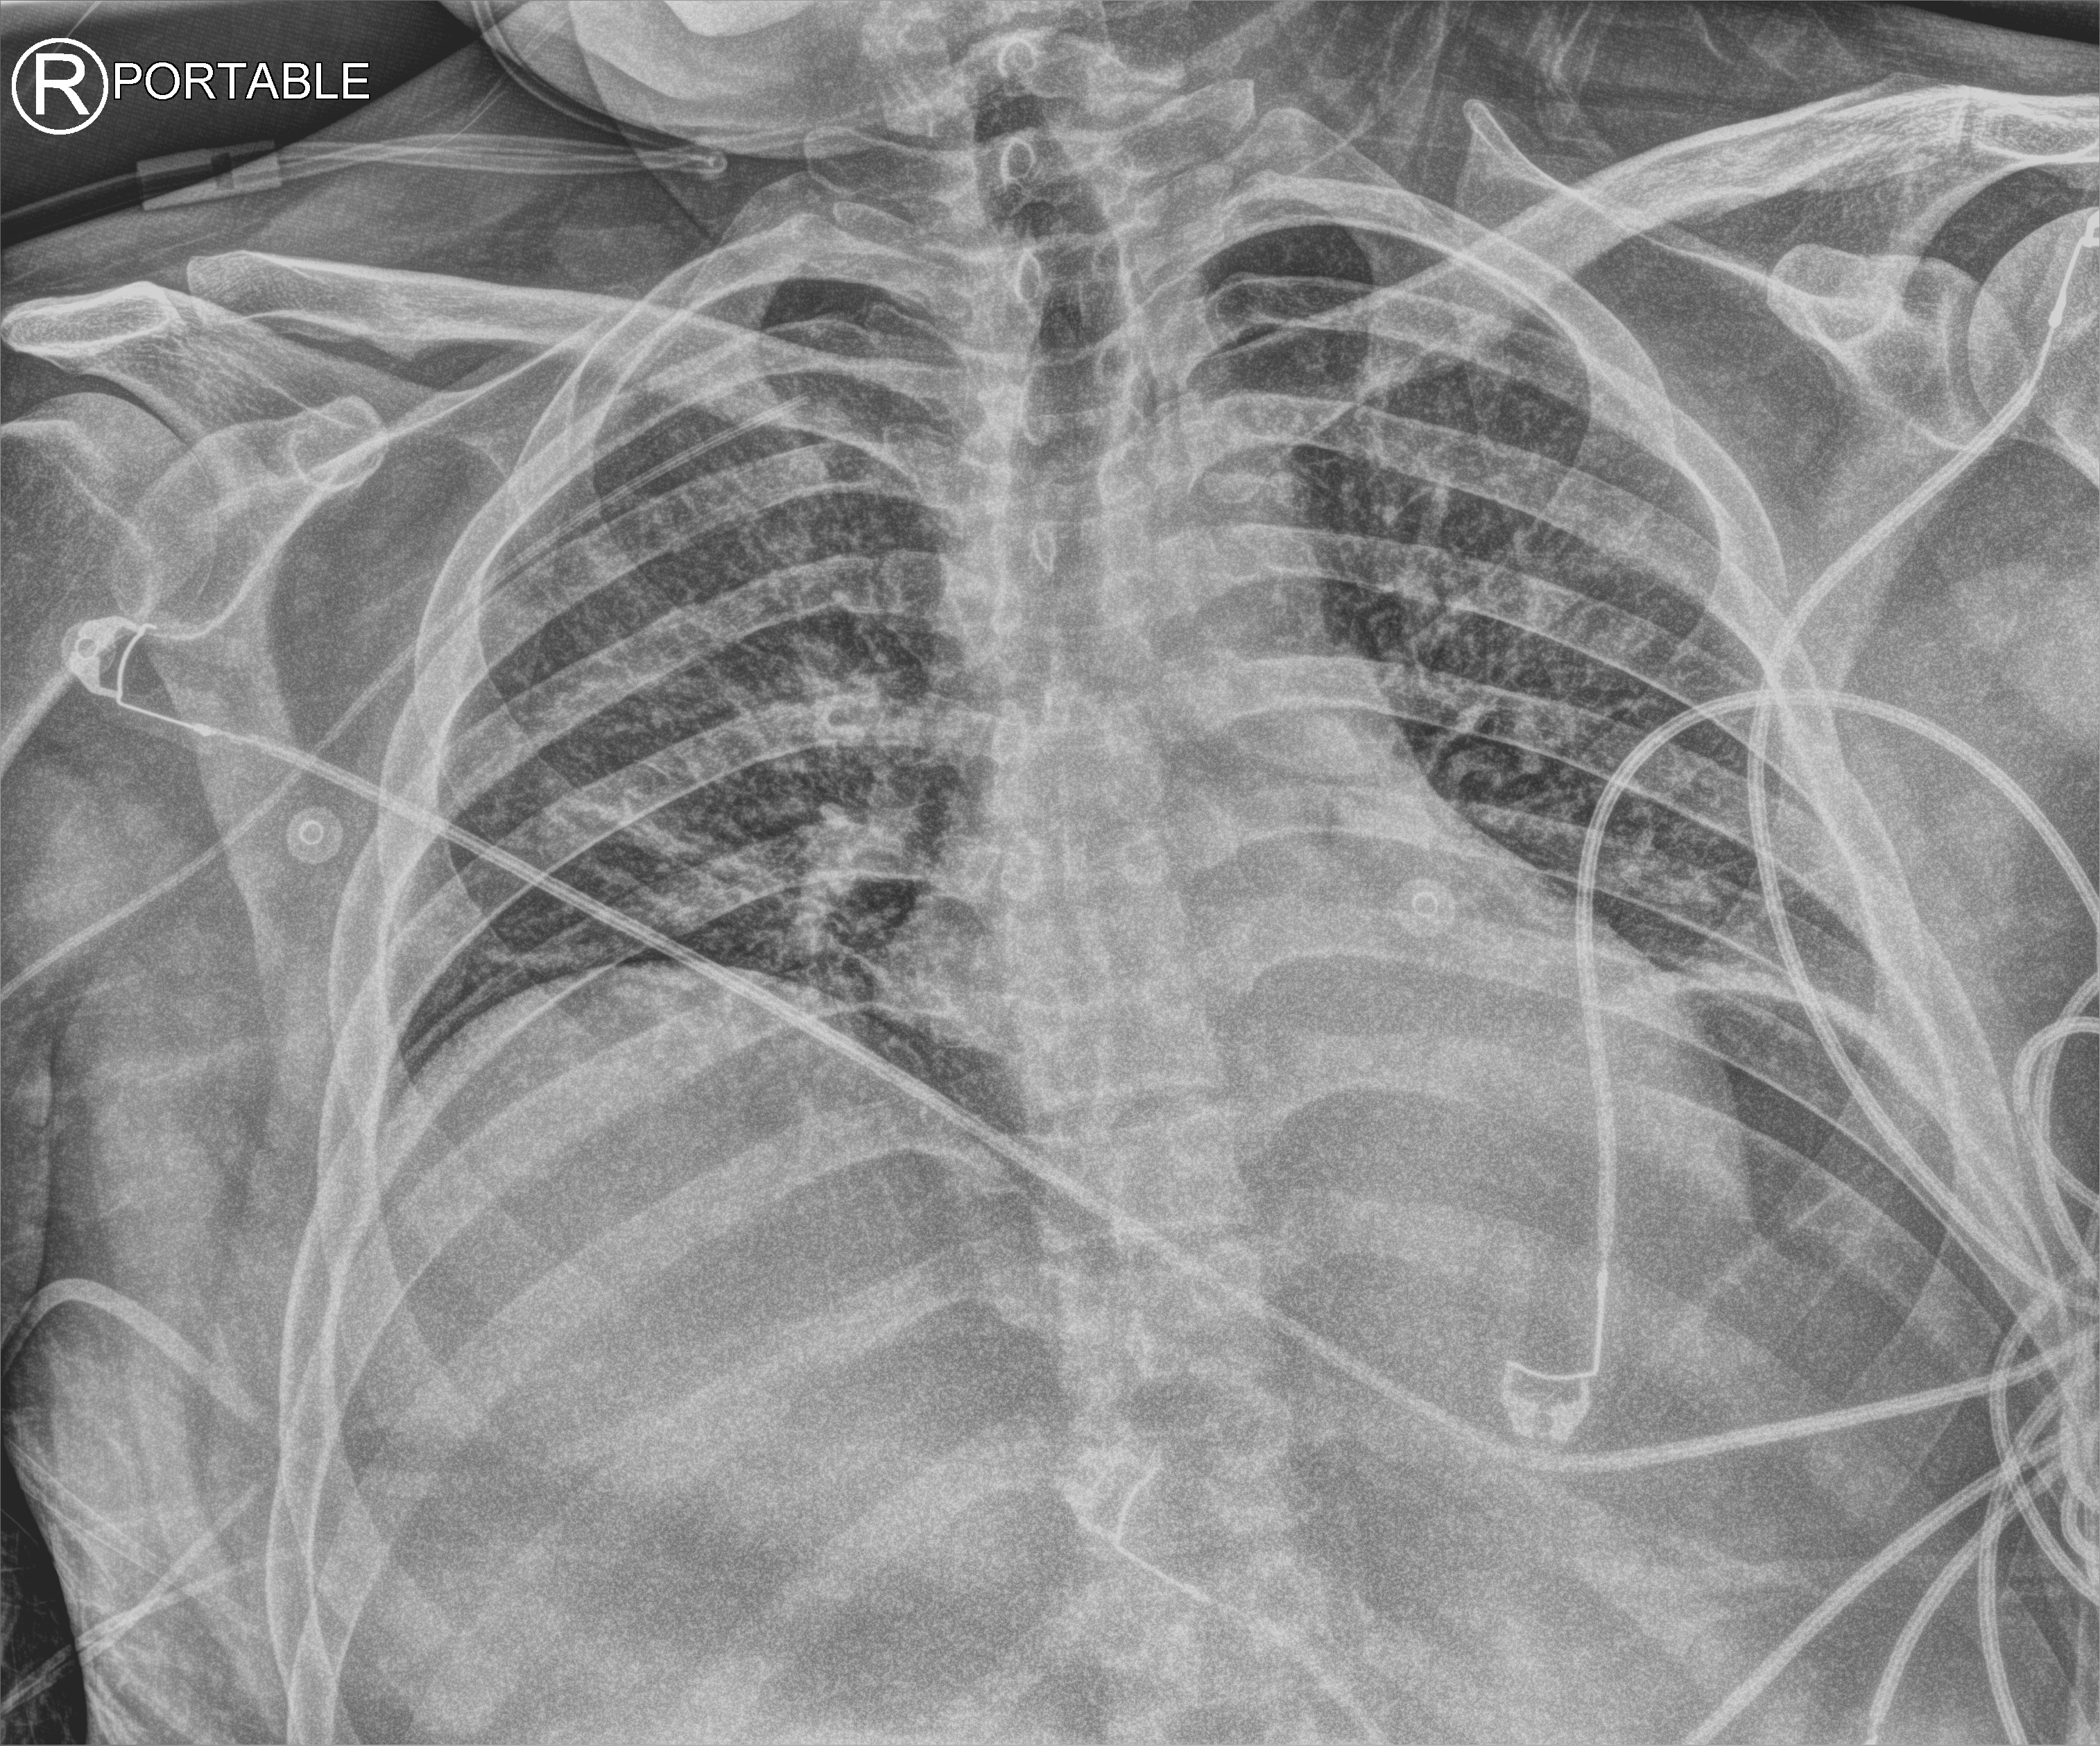
Portable chest radiograph, anteroposterior (AP) projection. Male patient hospitalised with COVID-19, age 18–59 years.
From the hospital-stay record, not from the radiograph (when in the stay this image was taken is not recorded): mechanically ventilated during this hospital stay: yes; admitted to intensive care during this hospital stay: yes.